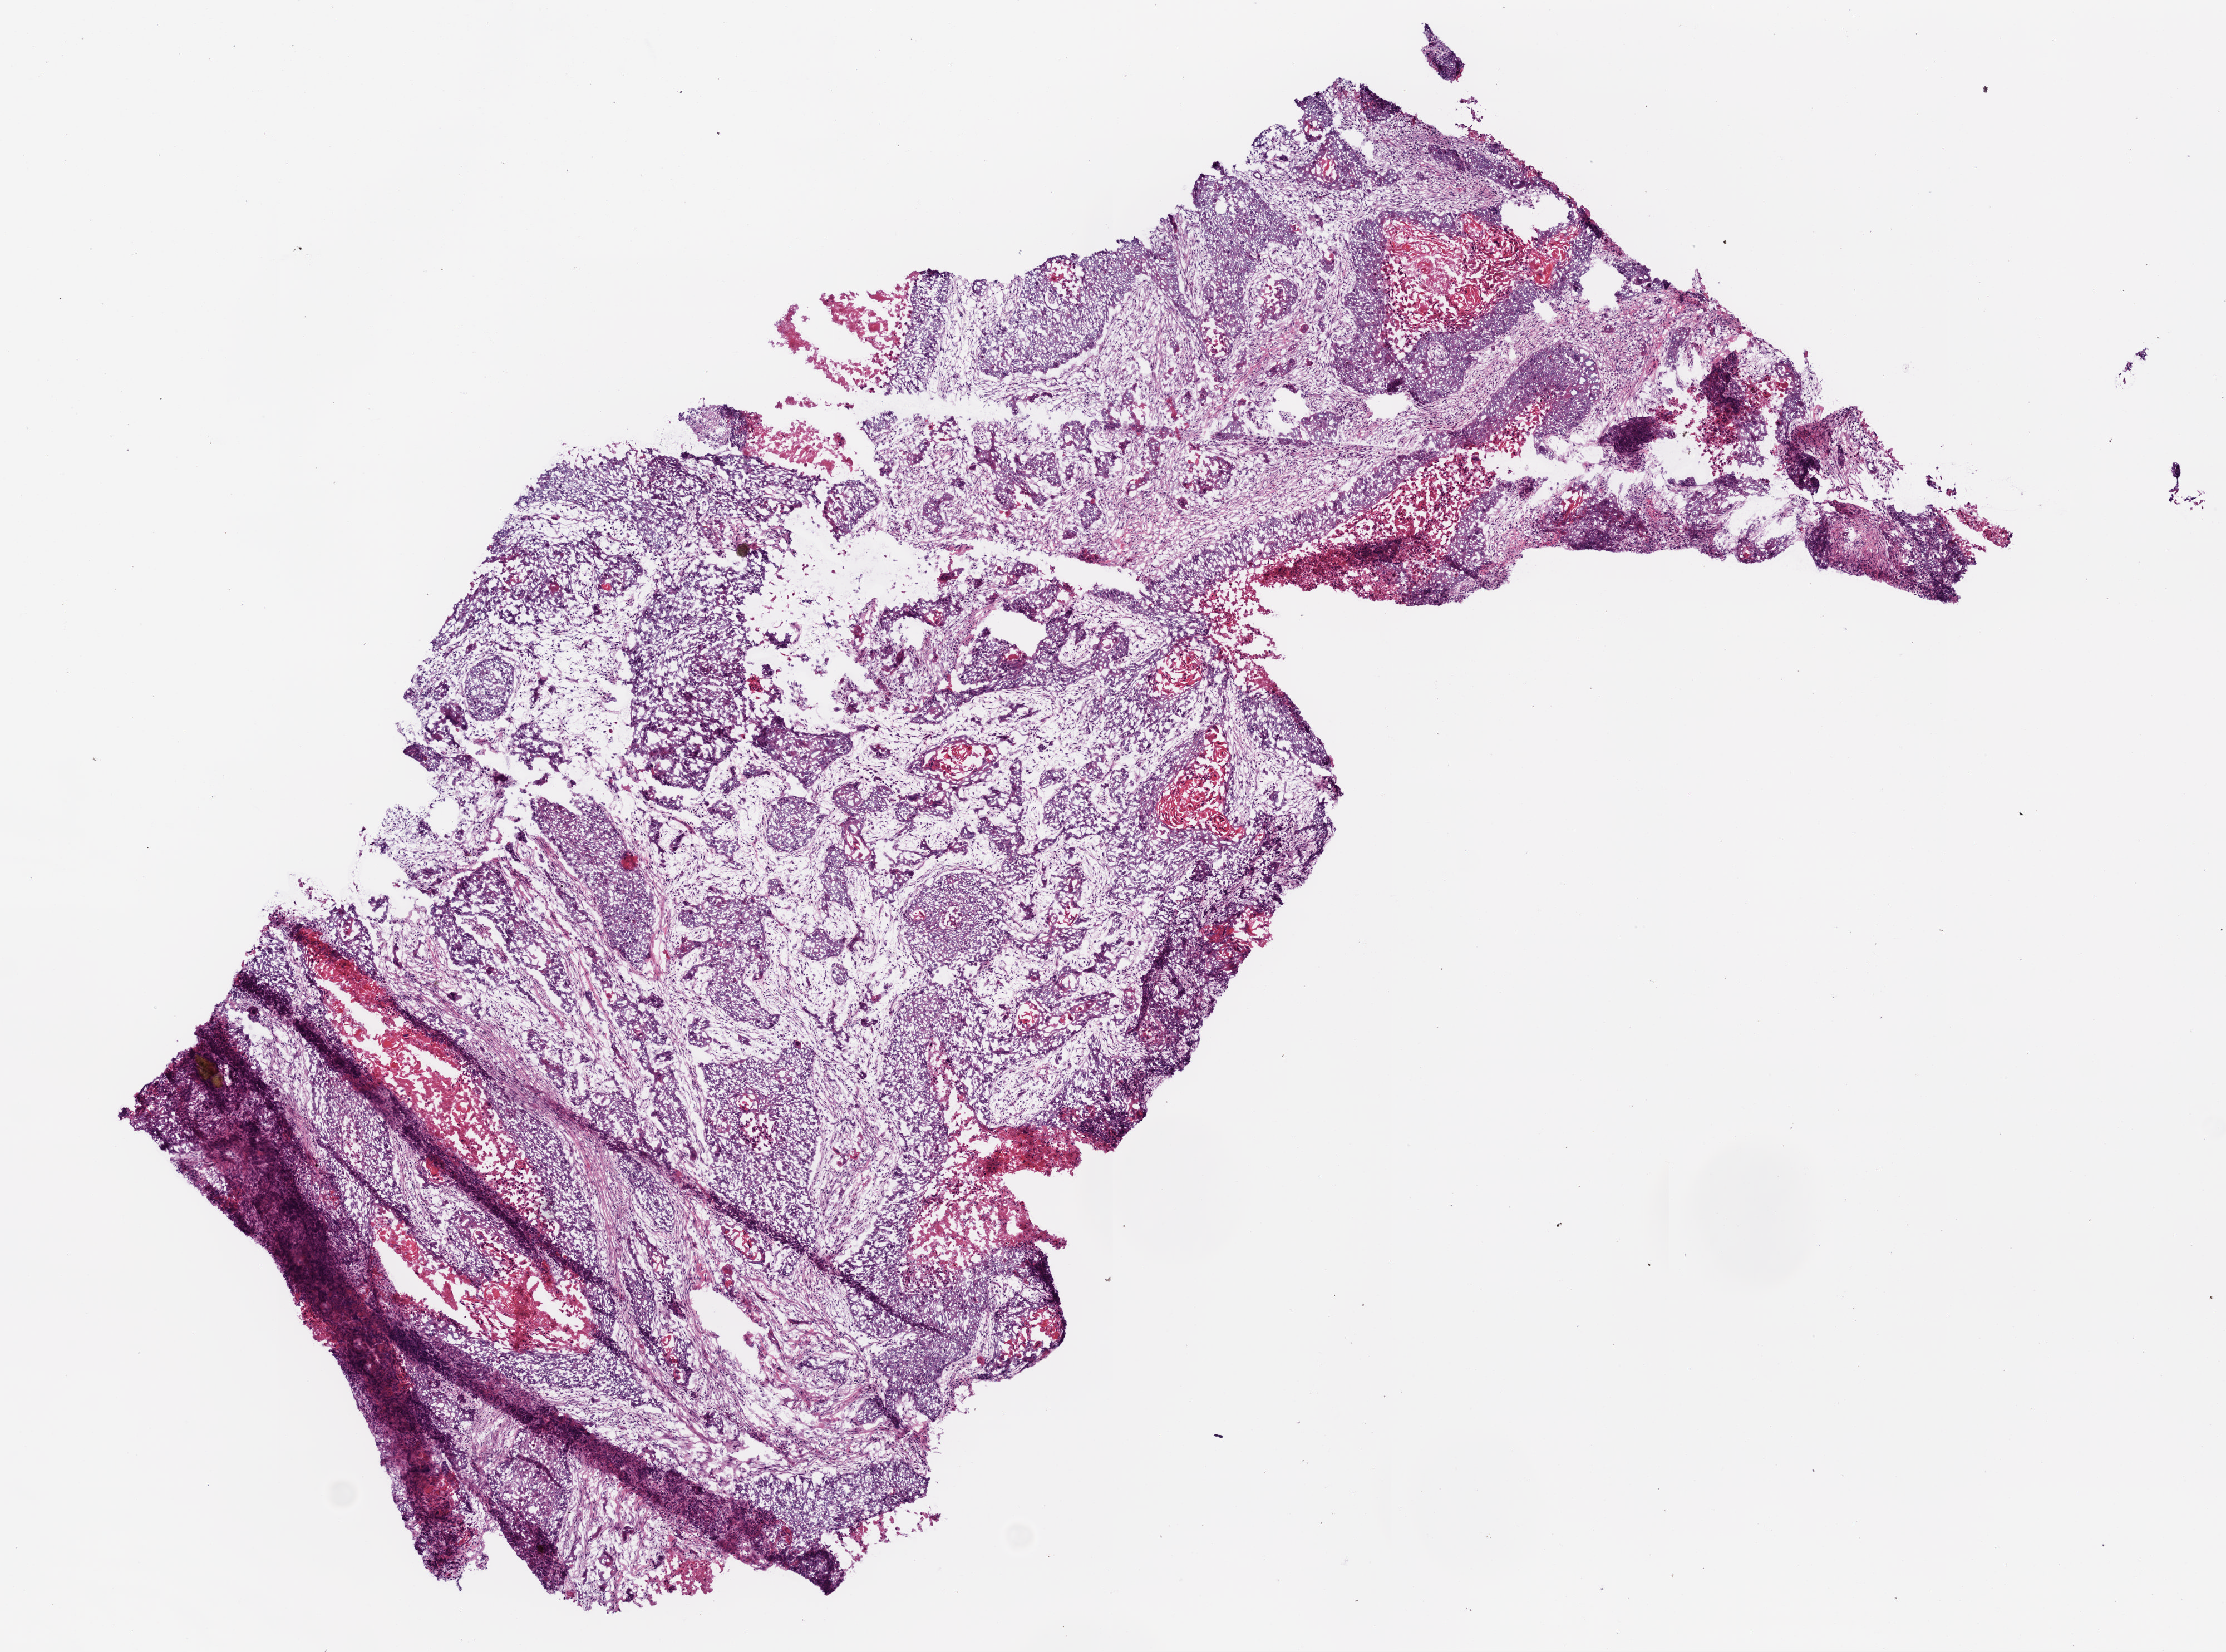
Hematoxylin and eosin (H&E) stained whole-slide image, shown as a low-resolution overview of the whole scanned area (about 8.0 x 6.0 mm, slide scanned at 20x); frozen section from the top of the tissue portion; primary tumour sample from the lung. Patient: male, age at initial diagnosis 55 years. Composition of this section per pathologist review: tumour cells 75%, tumour nuclei 85%, normal cells 0%, stromal cells 15%, necrosis 10%.
• AJCC pathologic stage: IIB
• histologic diagnosis: Squamous cell carcinoma, NOS (upper lobe, lung)